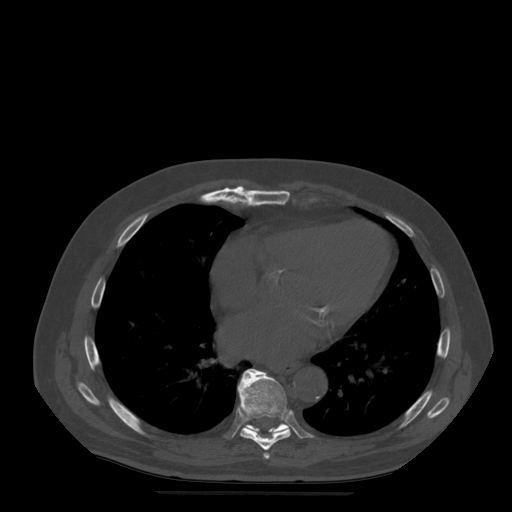
CT including the spine, one axial slice; position 306 of 522 along the scan axis; bone window (W 1800 / L 400 HU); 1.25 mm slice thickness; 512 × 512 image matrix, field of view 420 × 420 mm. Patient age 72 years. From the clinical record (not read from this slice): primary cancer: prostate.
Outlined on this slice (semi-automatically segmented with operator editing):
- T7 vertebra: bounding box (x1, y1, x2, y2) in pixels: (264, 453, 270, 459)
- T8 vertebra: (238, 370, 291, 451)
- T9 vertebra: (242, 369, 290, 434)